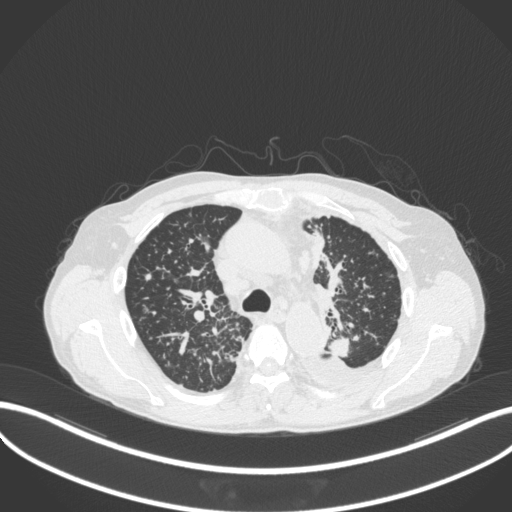
Chest CT, one axial slice; slice 251 of 319 in the series (ordered by position); reconstruction kernel B31f; 120 kVp; lung window (W 1500 / L -600 HU); 1 mm slice thickness; 512 × 512 image matrix, field of view 400 × 400 mm. Patient: male, 58 years. Case-level facts recorded for this patient, not image findings: clinical TNM (as recorded): T1c N3 M1.
Outlined on this slice (rectangle marked by the reading radiologist):
- lung tumour (recorded histology: adenocarcinoma): bounding box <326,334,353,361> (left, top, right, bottom; pixels)